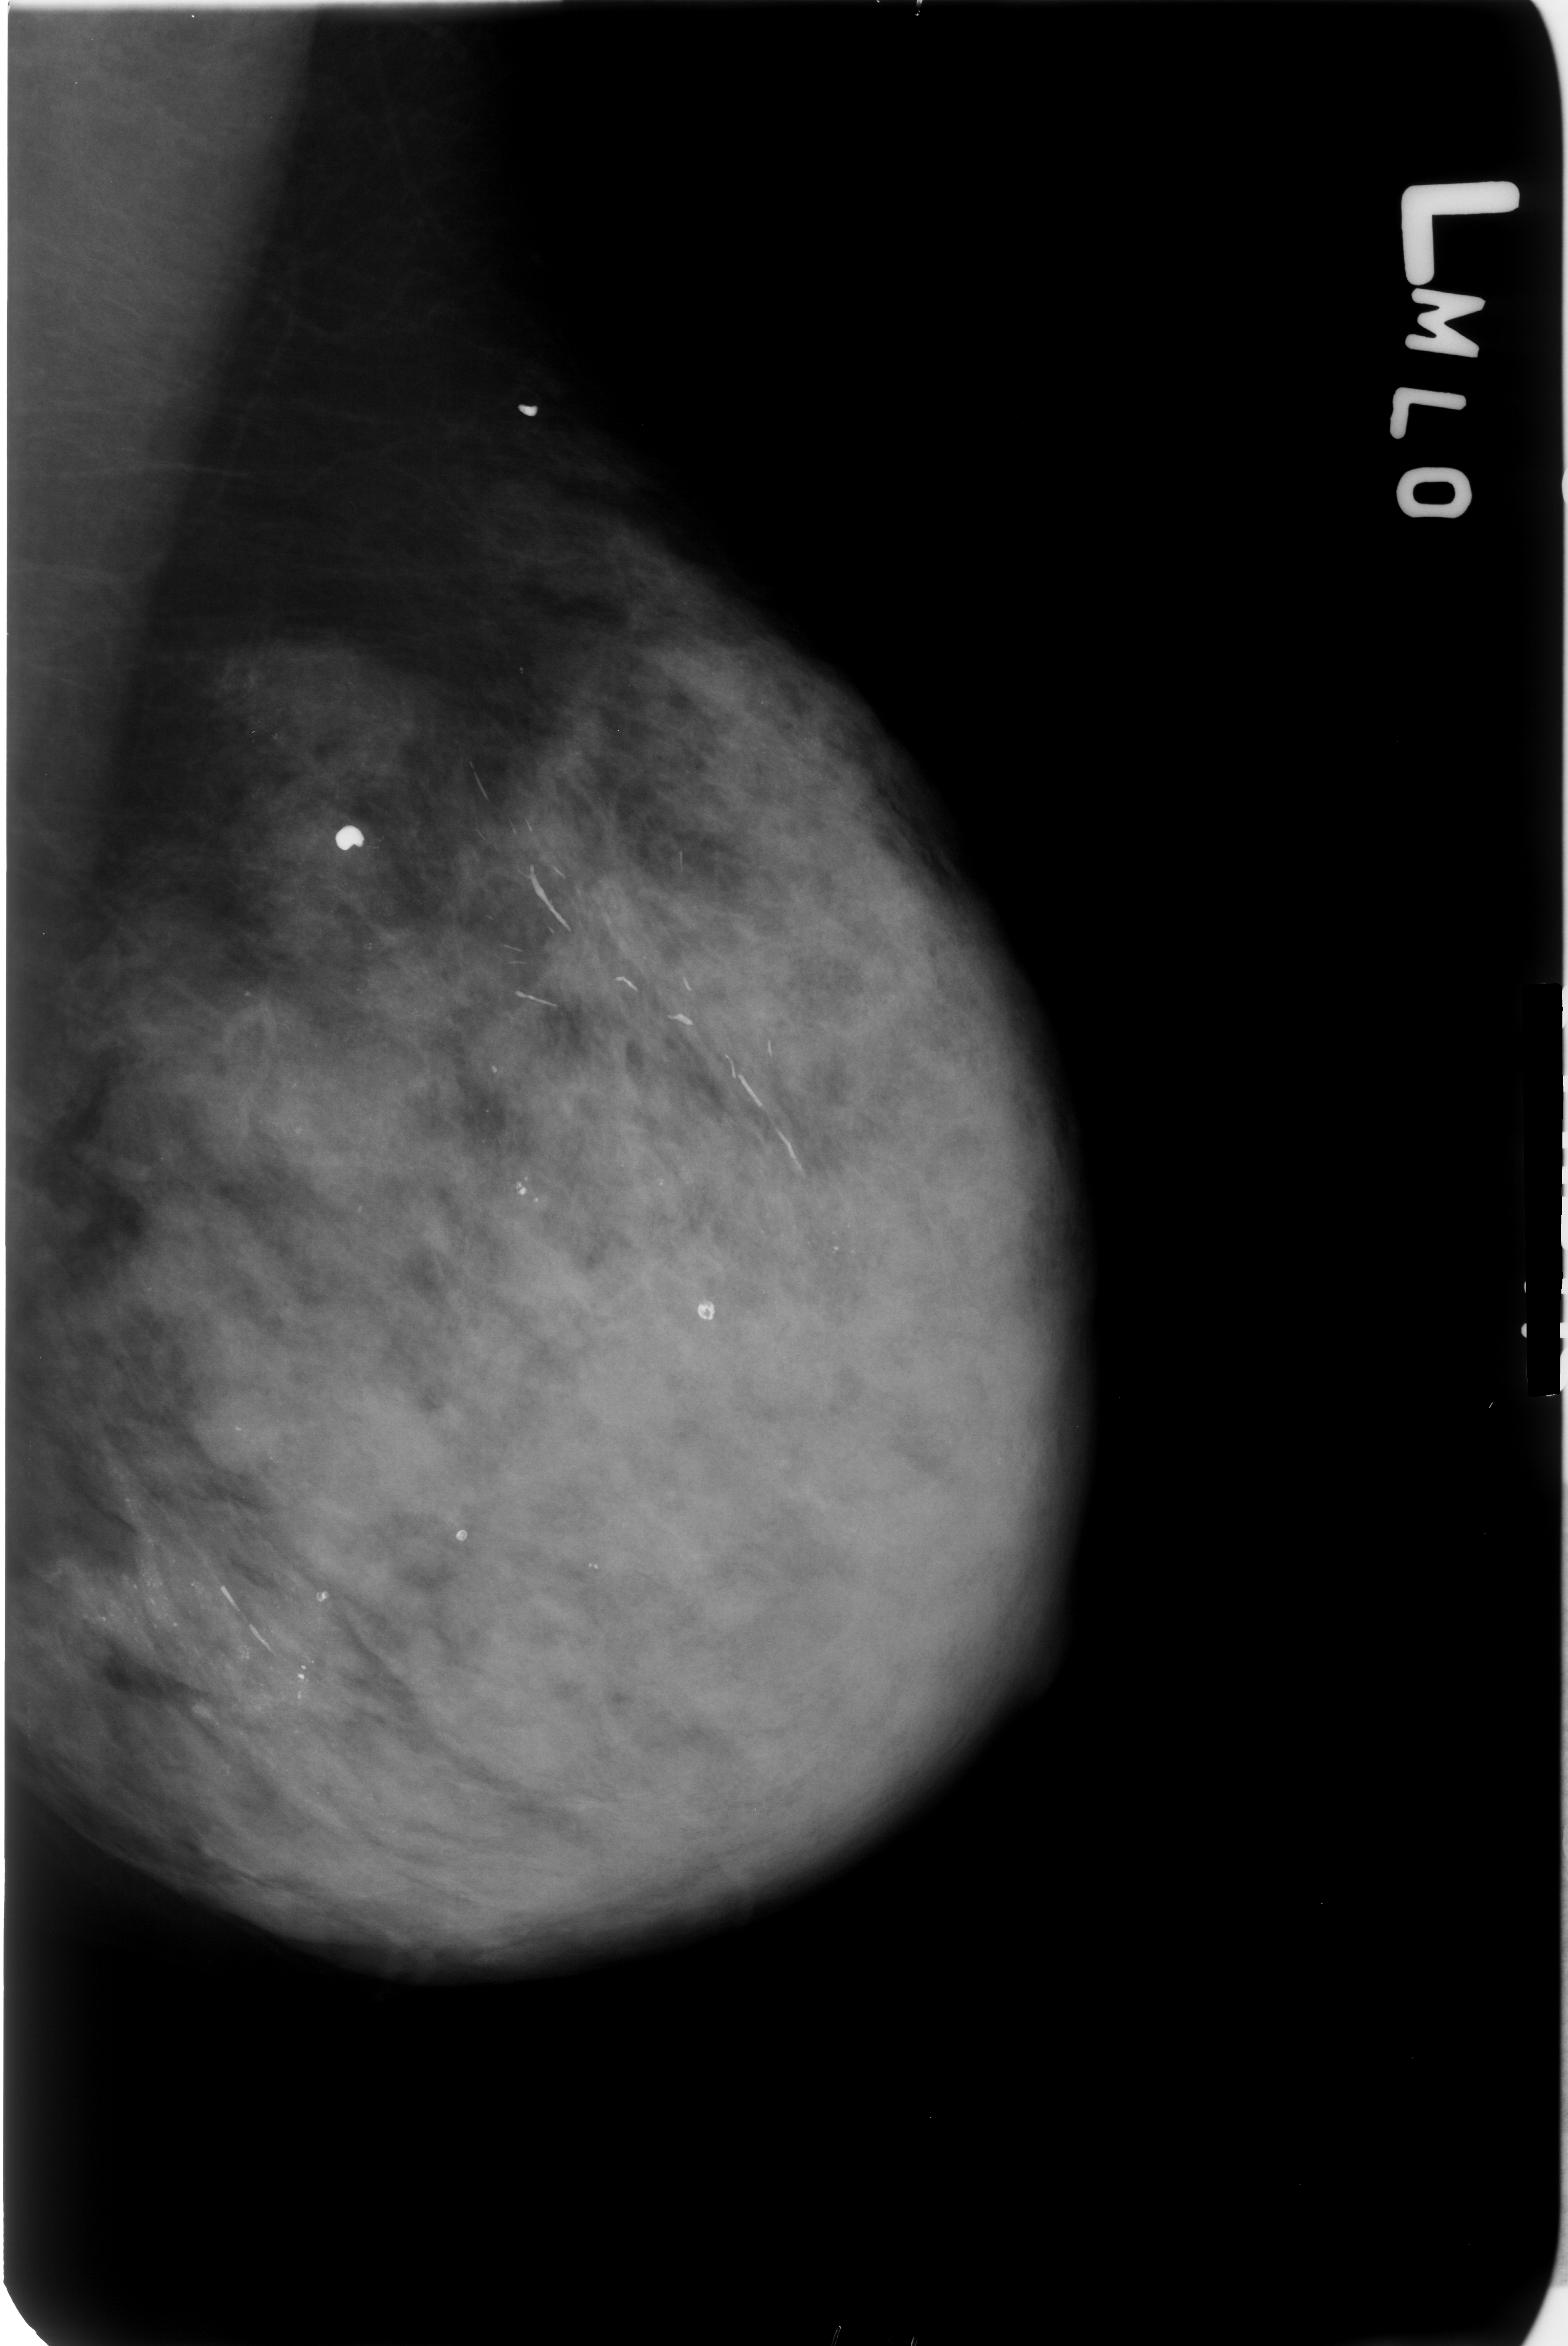
Digitized screen-film mammogram, left breast, MLO view, BI-RADS breast density category 4 (scale 1–4).
Abnormality record for this image: Finding 1 of 2: calcifications, morphology punctate / lucent center, distribution regional; BI-RADS assessment category 2; subtlety rating 5 on a 1 (subtle) to 5 (obvious) scale; benign; no additional work-up was recommended (benign without callback). Finding 2 of 2: calcifications, morphology punctate / lucent center, distribution regional; BI-RADS assessment category 2; benign; no additional work-up was recommended (benign without callback).